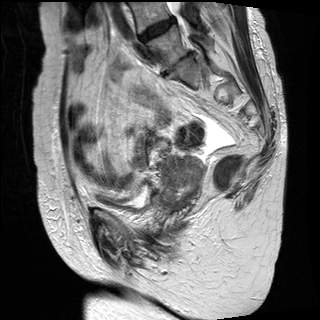
Pelvic MRI for cervical cancer, one sagittal slice. Position 11 of 30 along the scan axis. T2-weighted. 1.5 T. TE 89 ms, TR 2930 ms. 4 mm slice thickness. 320 × 320 image matrix, field of view 260 × 260 mm. Patient: female, 61 years.
Outlined on this slice (expert manual segmentation):
- uterus and cervix: bounding box (x1, y1, x2, y2) in pixels: (155, 153, 208, 214)